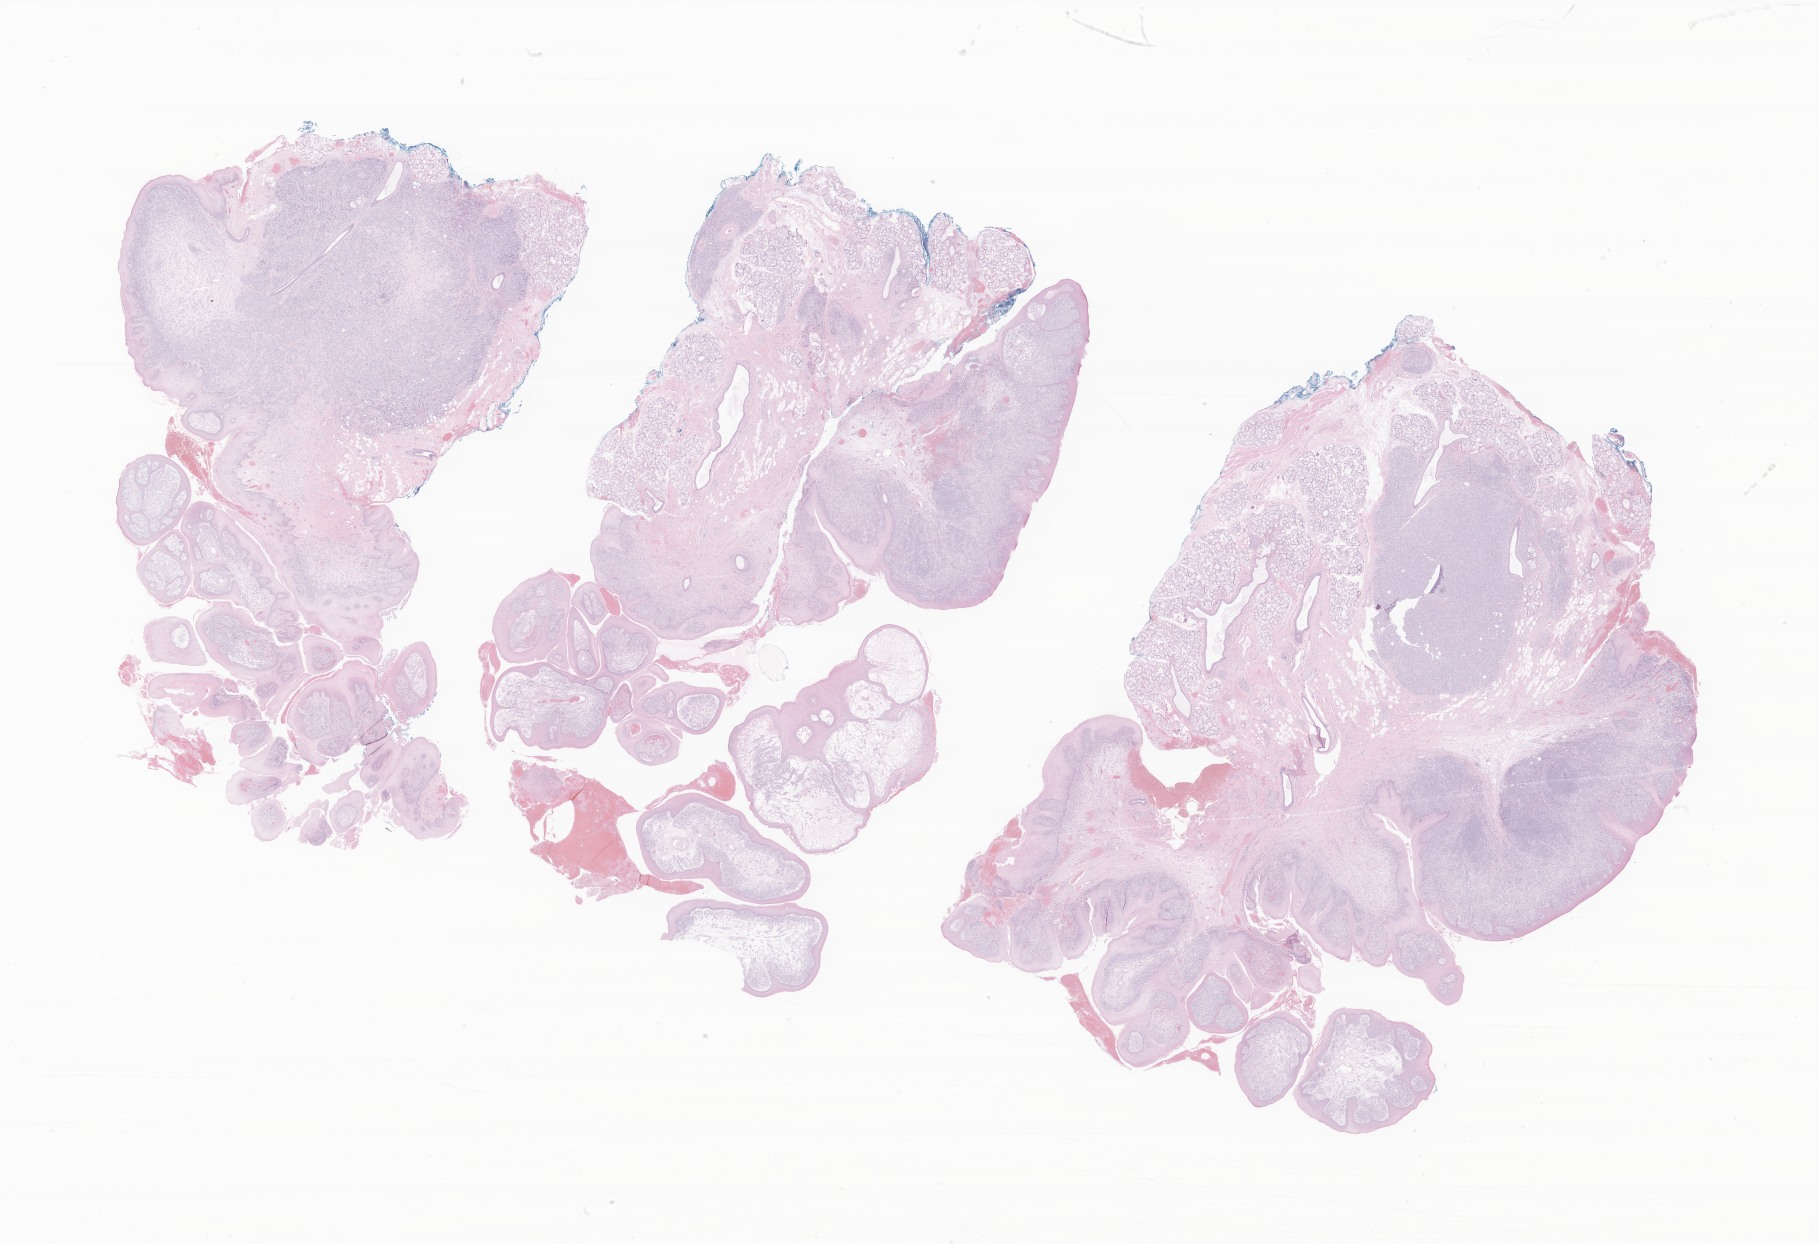
Whole-slide image, haematoxylin and eosin stain of tumor tissue from the soft palate — a low-resolution overview of the entire scanned area, about 30.7 x 21.0 mm. Formalin-fixed paraffin-embedded section. Patient female; age 192 months (16 years).
Diagnosis: Embryonal rhabdomyosarcoma, NOS.